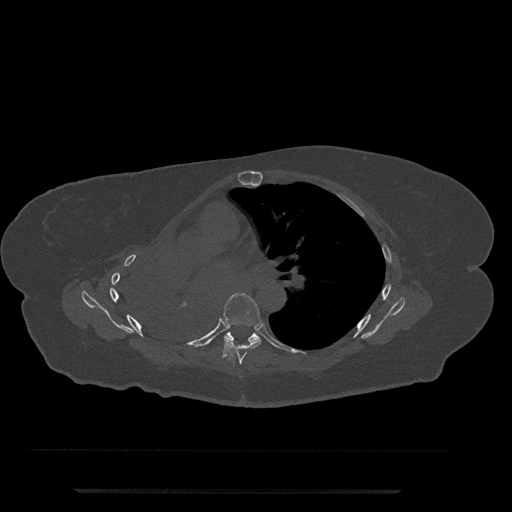
CT including the spine, one axial slice; position 476 of 797 along the scan axis; bone window (W 1800 / L 400 HU); 512 × 512 image matrix. Patient: female, 51 years. Case-level facts recorded for this patient, not image findings: primary cancer: neuro.
Annotated regions visible in this slice (semi-automatically segmented with operator editing):
- T6 vertebra: bounding box <222,293,262,365> (left, top, right, bottom; pixels)
- T7 vertebra: <224,332,261,341>